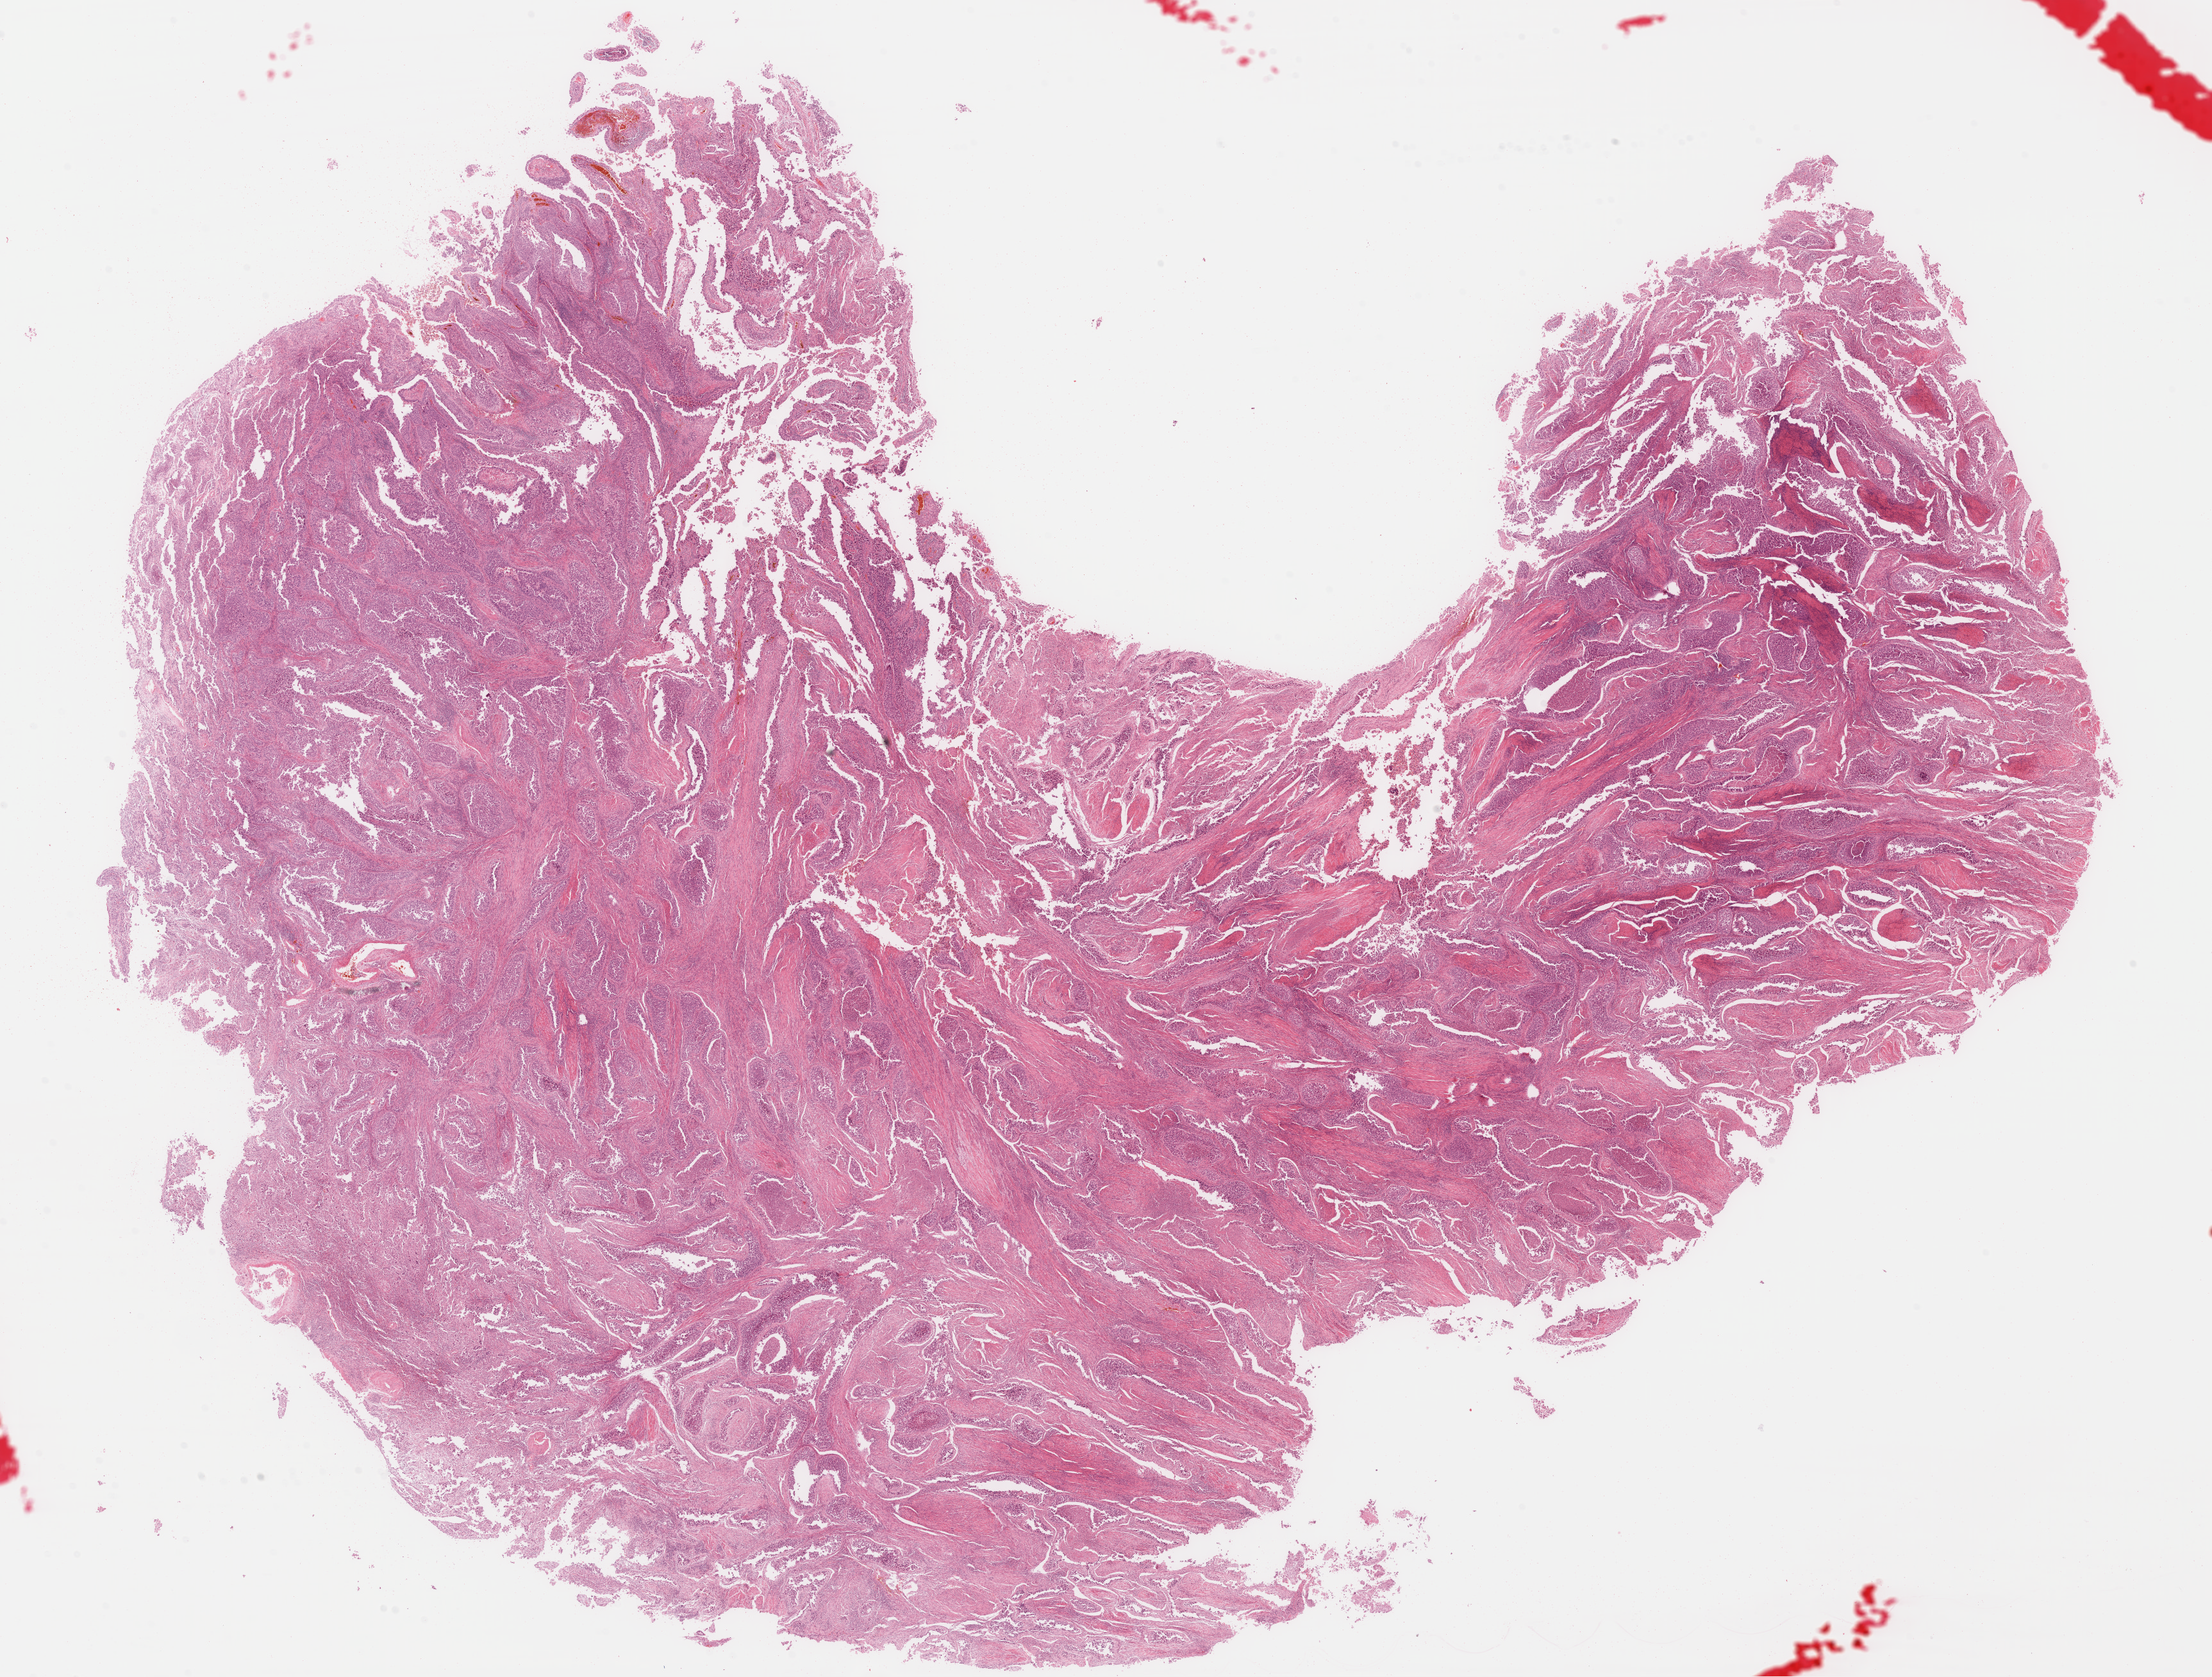
H&E-stained whole-slide image — whole scanned area (about 27.1 x 20.6 mm, acquisition: 40x scan) shown as a low-resolution overview, formalin-fixed paraffin-embedded (FFPE) diagnostic section, sample: primary tumour, bladder. Male, age 66 years at initial diagnosis.
Diagnosis: Papillary transitional cell carcinoma.